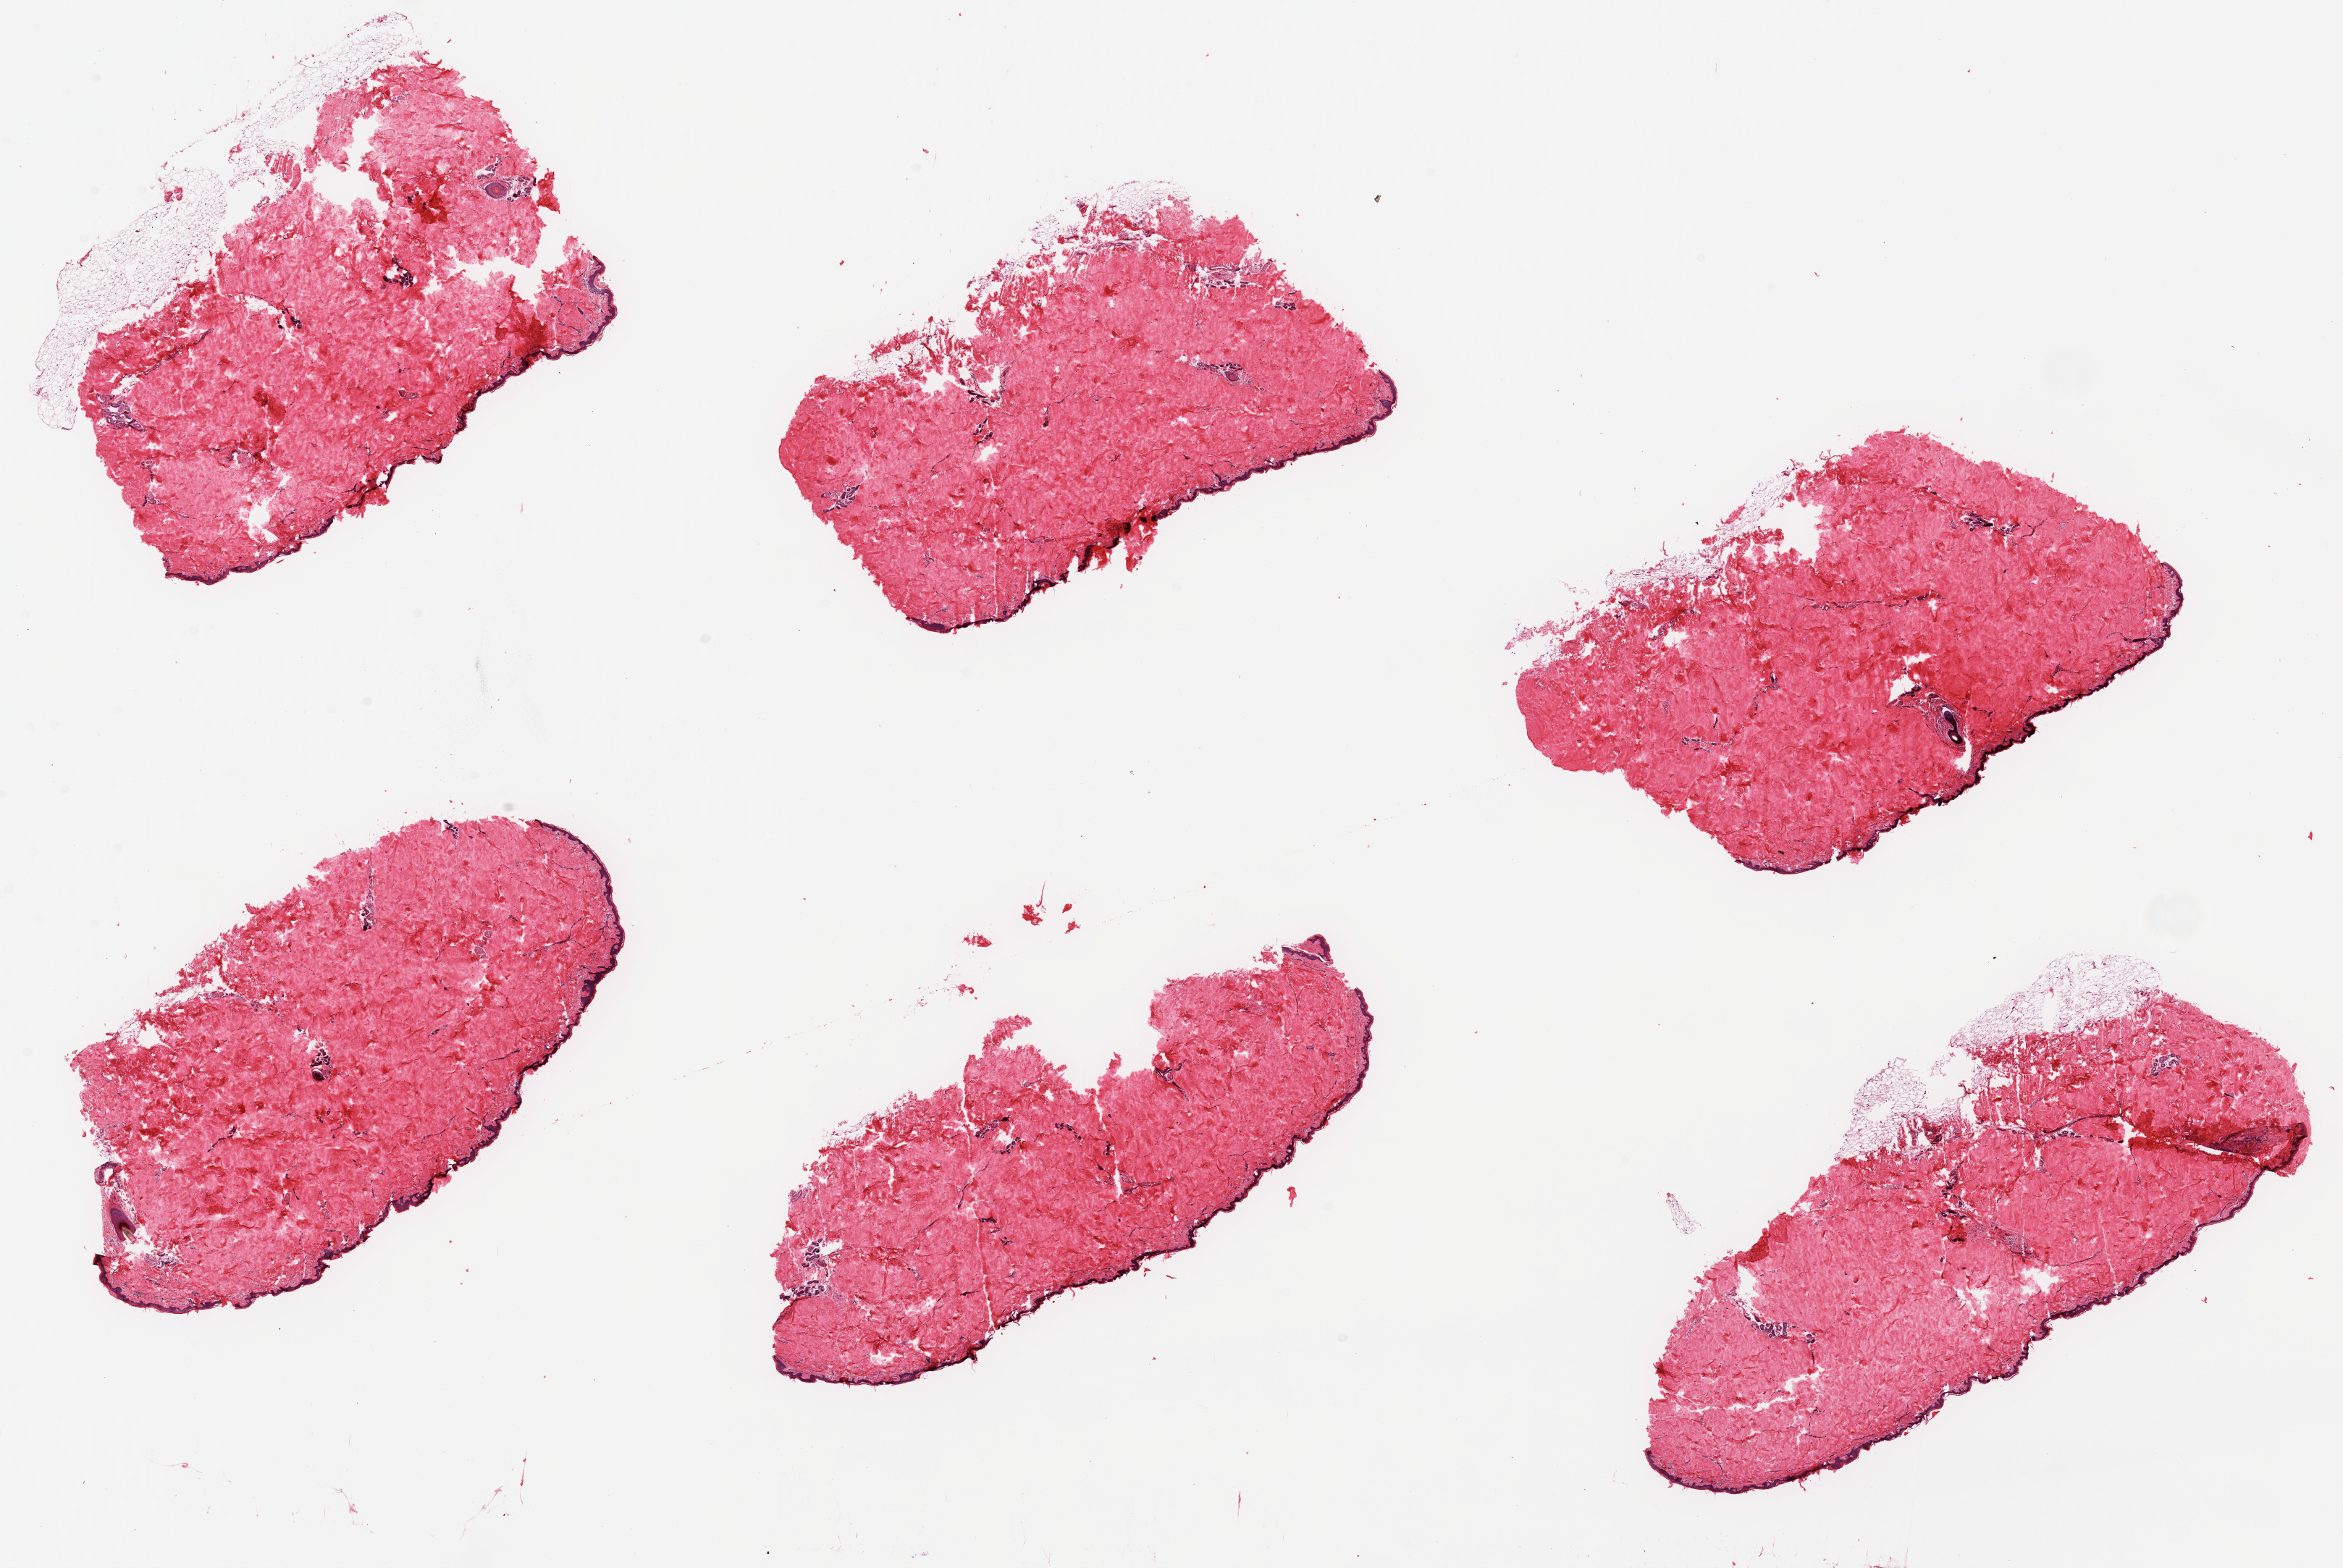
Whole-slide image, haematoxylin and eosin stain, brightfield, low-resolution overview of the scanned area, about 25.6 x 17.1 mm (from a 20x scan), PAXgene-fixed paraffin-embedded (PFPE) section, section of skin of suprapubic region (target tissue), tissue donor sample. Donor: male.
• review note (as recorded): 6 pieces; few pieces include up to 20% attached fat